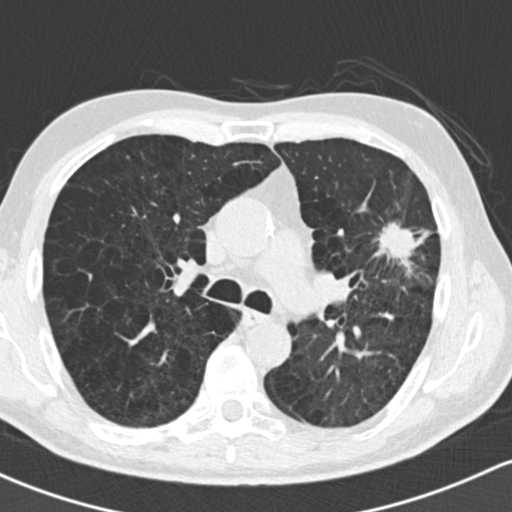
Low-dose screening chest CT, one axial slice; position 97 of 162 along the scan axis; reconstruction kernel B30f; 120 kVp; lung window (W 1500 / L -600 HU); 2 mm slice thickness; 512 × 512 image matrix, field of view 318 × 318 mm.
Annotated regions visible in this slice (expert manual segmentation):
- lesion 1 (tumor, upper lobe of left lung): bounding box (x1, y1, x2, y2) in pixels: (379, 222, 419, 273)